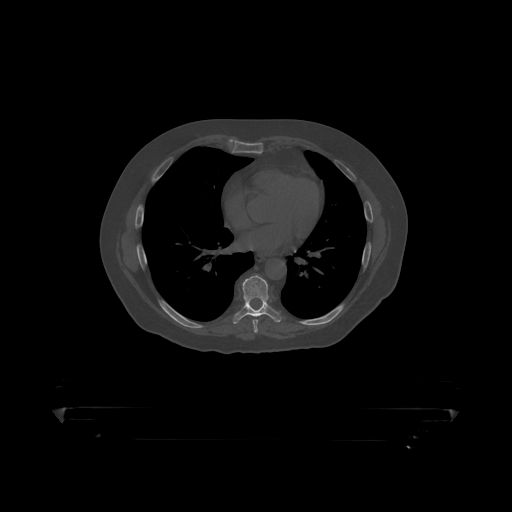
CT including the spine, one axial slice; position 261 of 390 along the scan axis; reconstruction kernel STANDARD; 120 kVp; bone window (W 1800 / L 400 HU); 1.25 mm slice thickness; 512 × 512 image matrix, field of view 650 × 650 mm. Male patient, age 60 years. Case-level facts recorded for this patient, not image findings: primary cancer: prostate.
Outlined on this slice (semi-automatically segmented with operator editing):
- T8 vertebra: box from (x=235, y=275) to (x=279, y=318) px